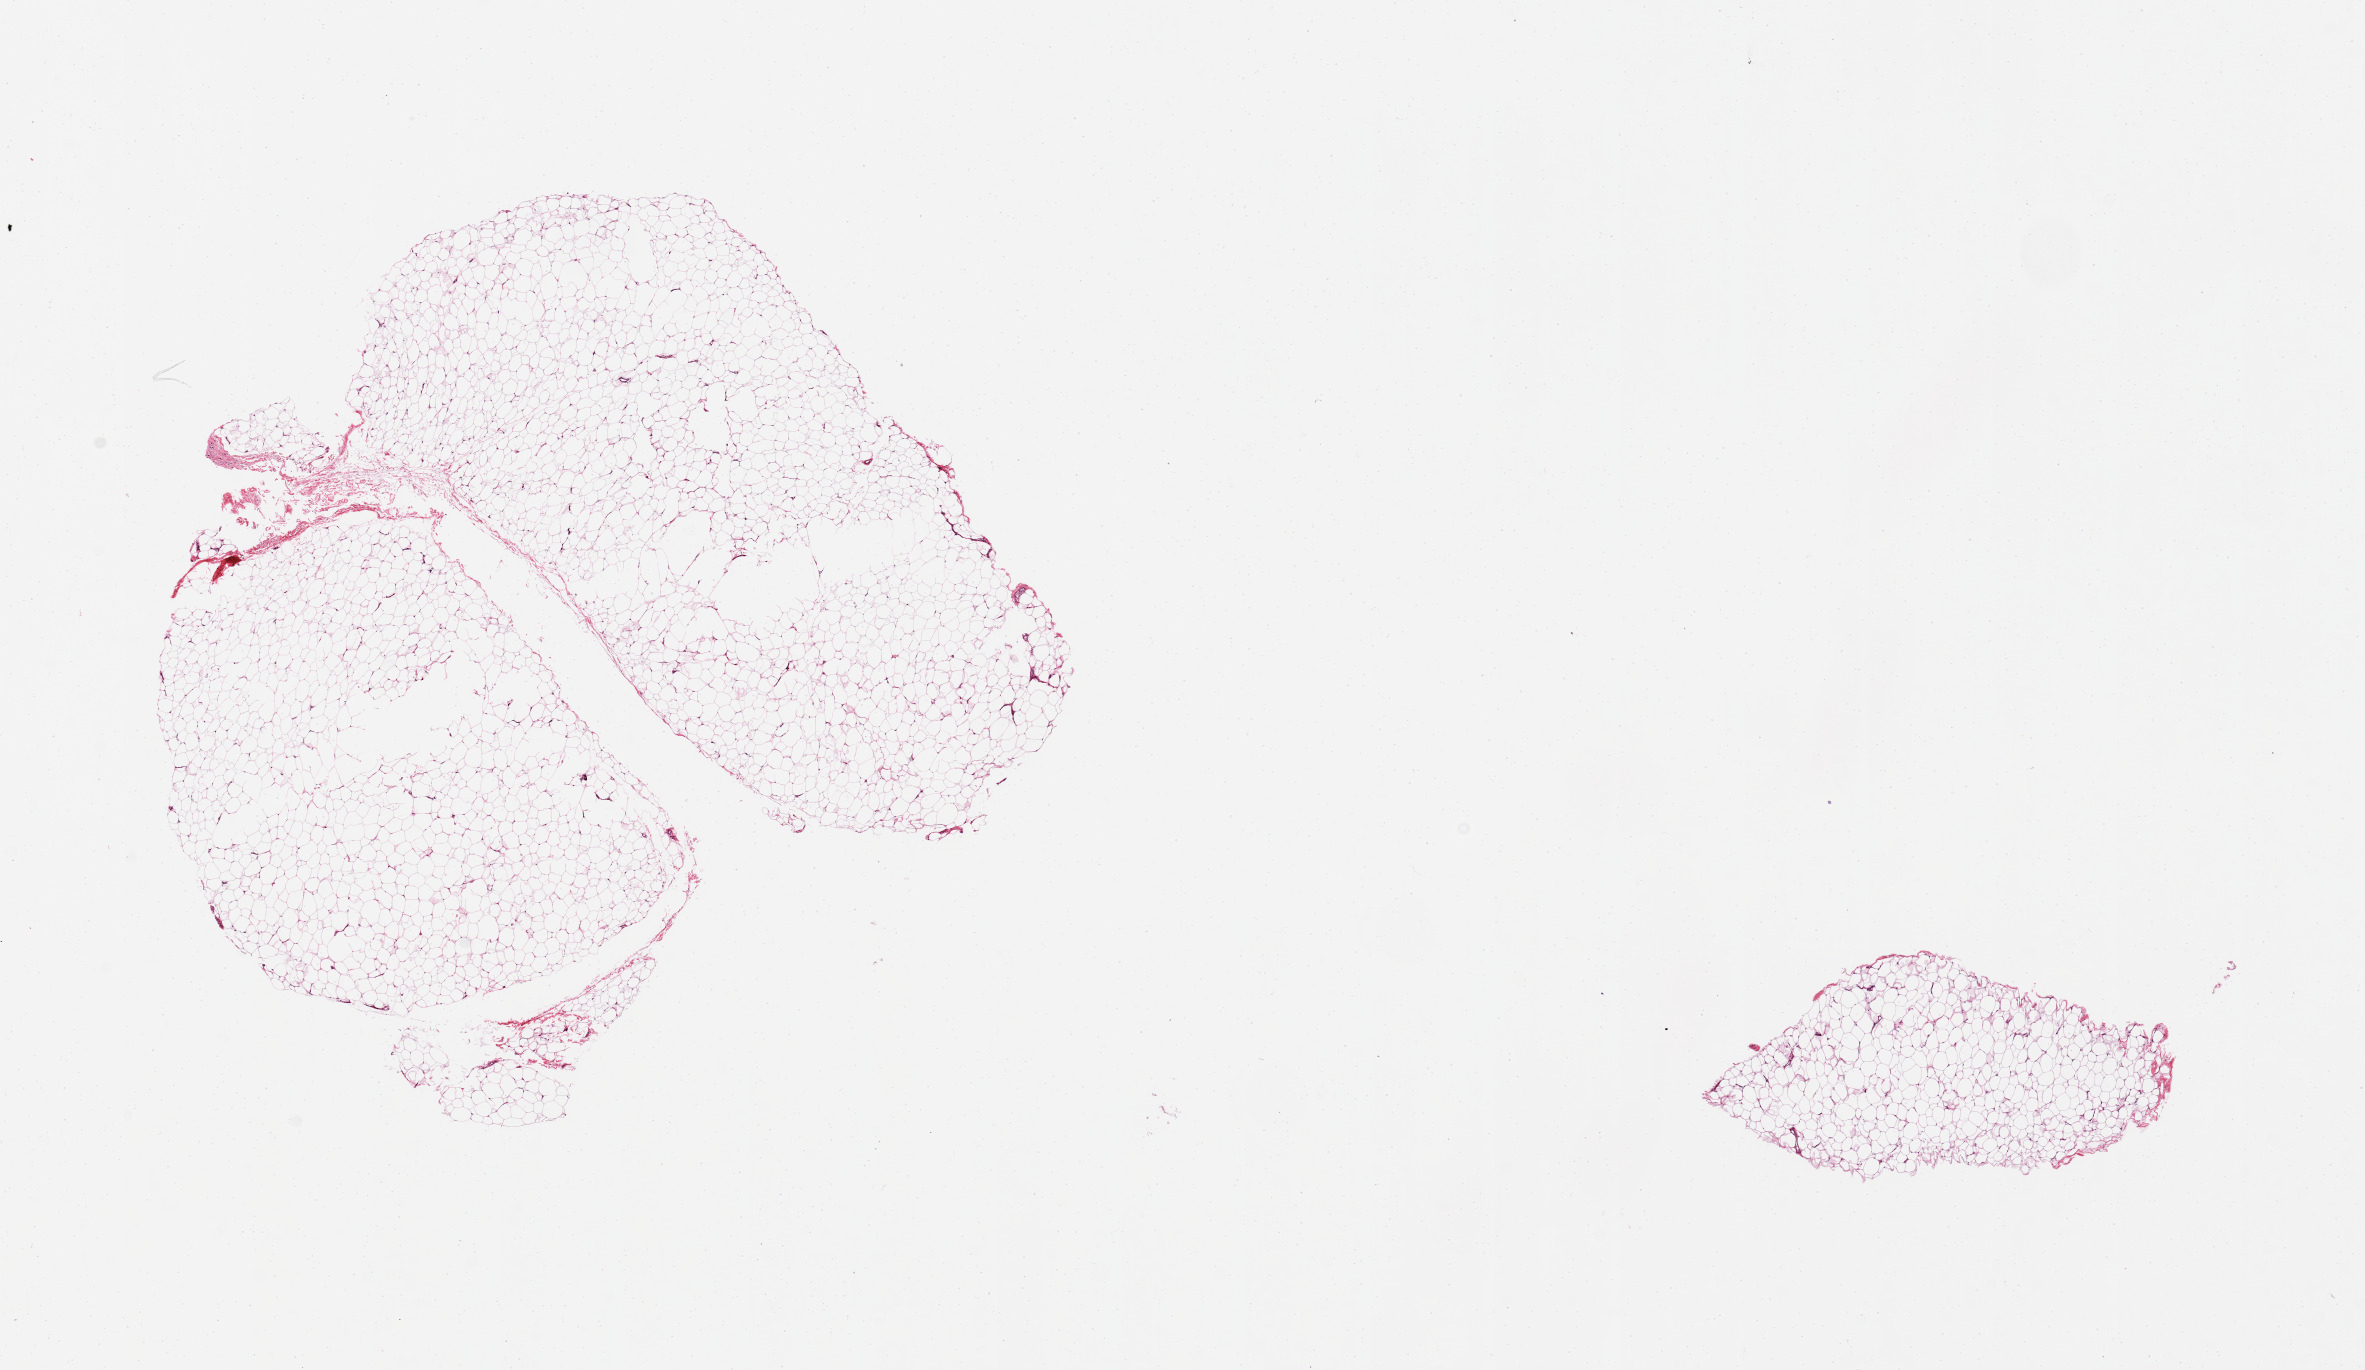
H&E whole-slide image, brightfield, a low-resolution overview of the entire scanned area, about 18.7 x 10.8 mm, PAXgene-fixed paraffin-embedded (PFPE) section, sampled site (target tissue): adipose tissue, tissue donor sample.
Review note (as recorded): 2 pieces.